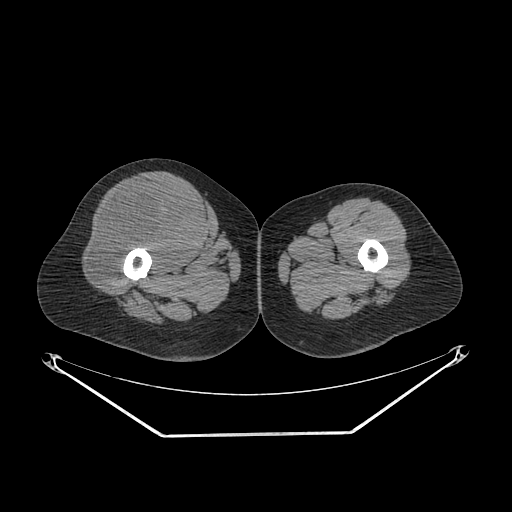
CT of an extremity soft-tissue mass (from a PET/CT study), one axial slice. Slice 254 of 311 in the series (ordered by position). Soft-tissue window (W 400 / L 40 HU). 3.75 mm slice thickness. 512 × 512 image matrix, field of view 500 × 500 mm. Female patient. Case-level facts recorded for this patient, not image findings: histological type: pleiomorphic undifferentiated sarcoma; grade: high; site of the primary tumour: right quadricep.
Annotated regions visible in this slice (expert contour drawn on MRI and transferred to this co-registered scan by the dataset authors):
- tumour plus oedema (research contour): bounding box <91,183,200,289> (left, top, right, bottom; pixels)
- tumour (research contour): <91,183,200,289>